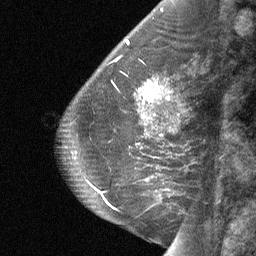
Breast MRI (dynamic contrast-enhanced), one sagittal slice; position 24 of 64 along the scan axis; dynamic contrast-enhanced study with each time point stored as its own series, time point 2 of 3 at this slice position (early post-contrast, ordered by acquisition time); 1.5 T; TE 4.8 ms, TR 27 ms; 2 mm slice thickness; 256 × 256 image matrix, field of view 180 × 180 mm. Patient: female, 59 years. Case-level facts recorded for this patient, not image findings: setting: breast cancer imaged before/during neoadjuvant chemotherapy; receptor status: triple-negative.
Outlined on this slice (semi-automatic segmentation, software-assisted and operator-edited):
- analysis volume of interest (the breast-tissue region the enhancement analysis was run in; not a lesion): bounding box <130,75,173,114> (left, top, right, bottom; pixels)
- tumour enhancement mask (voxels above the 90 % enhancement threshold inside the analysis volume of interest): <138,81,169,103>